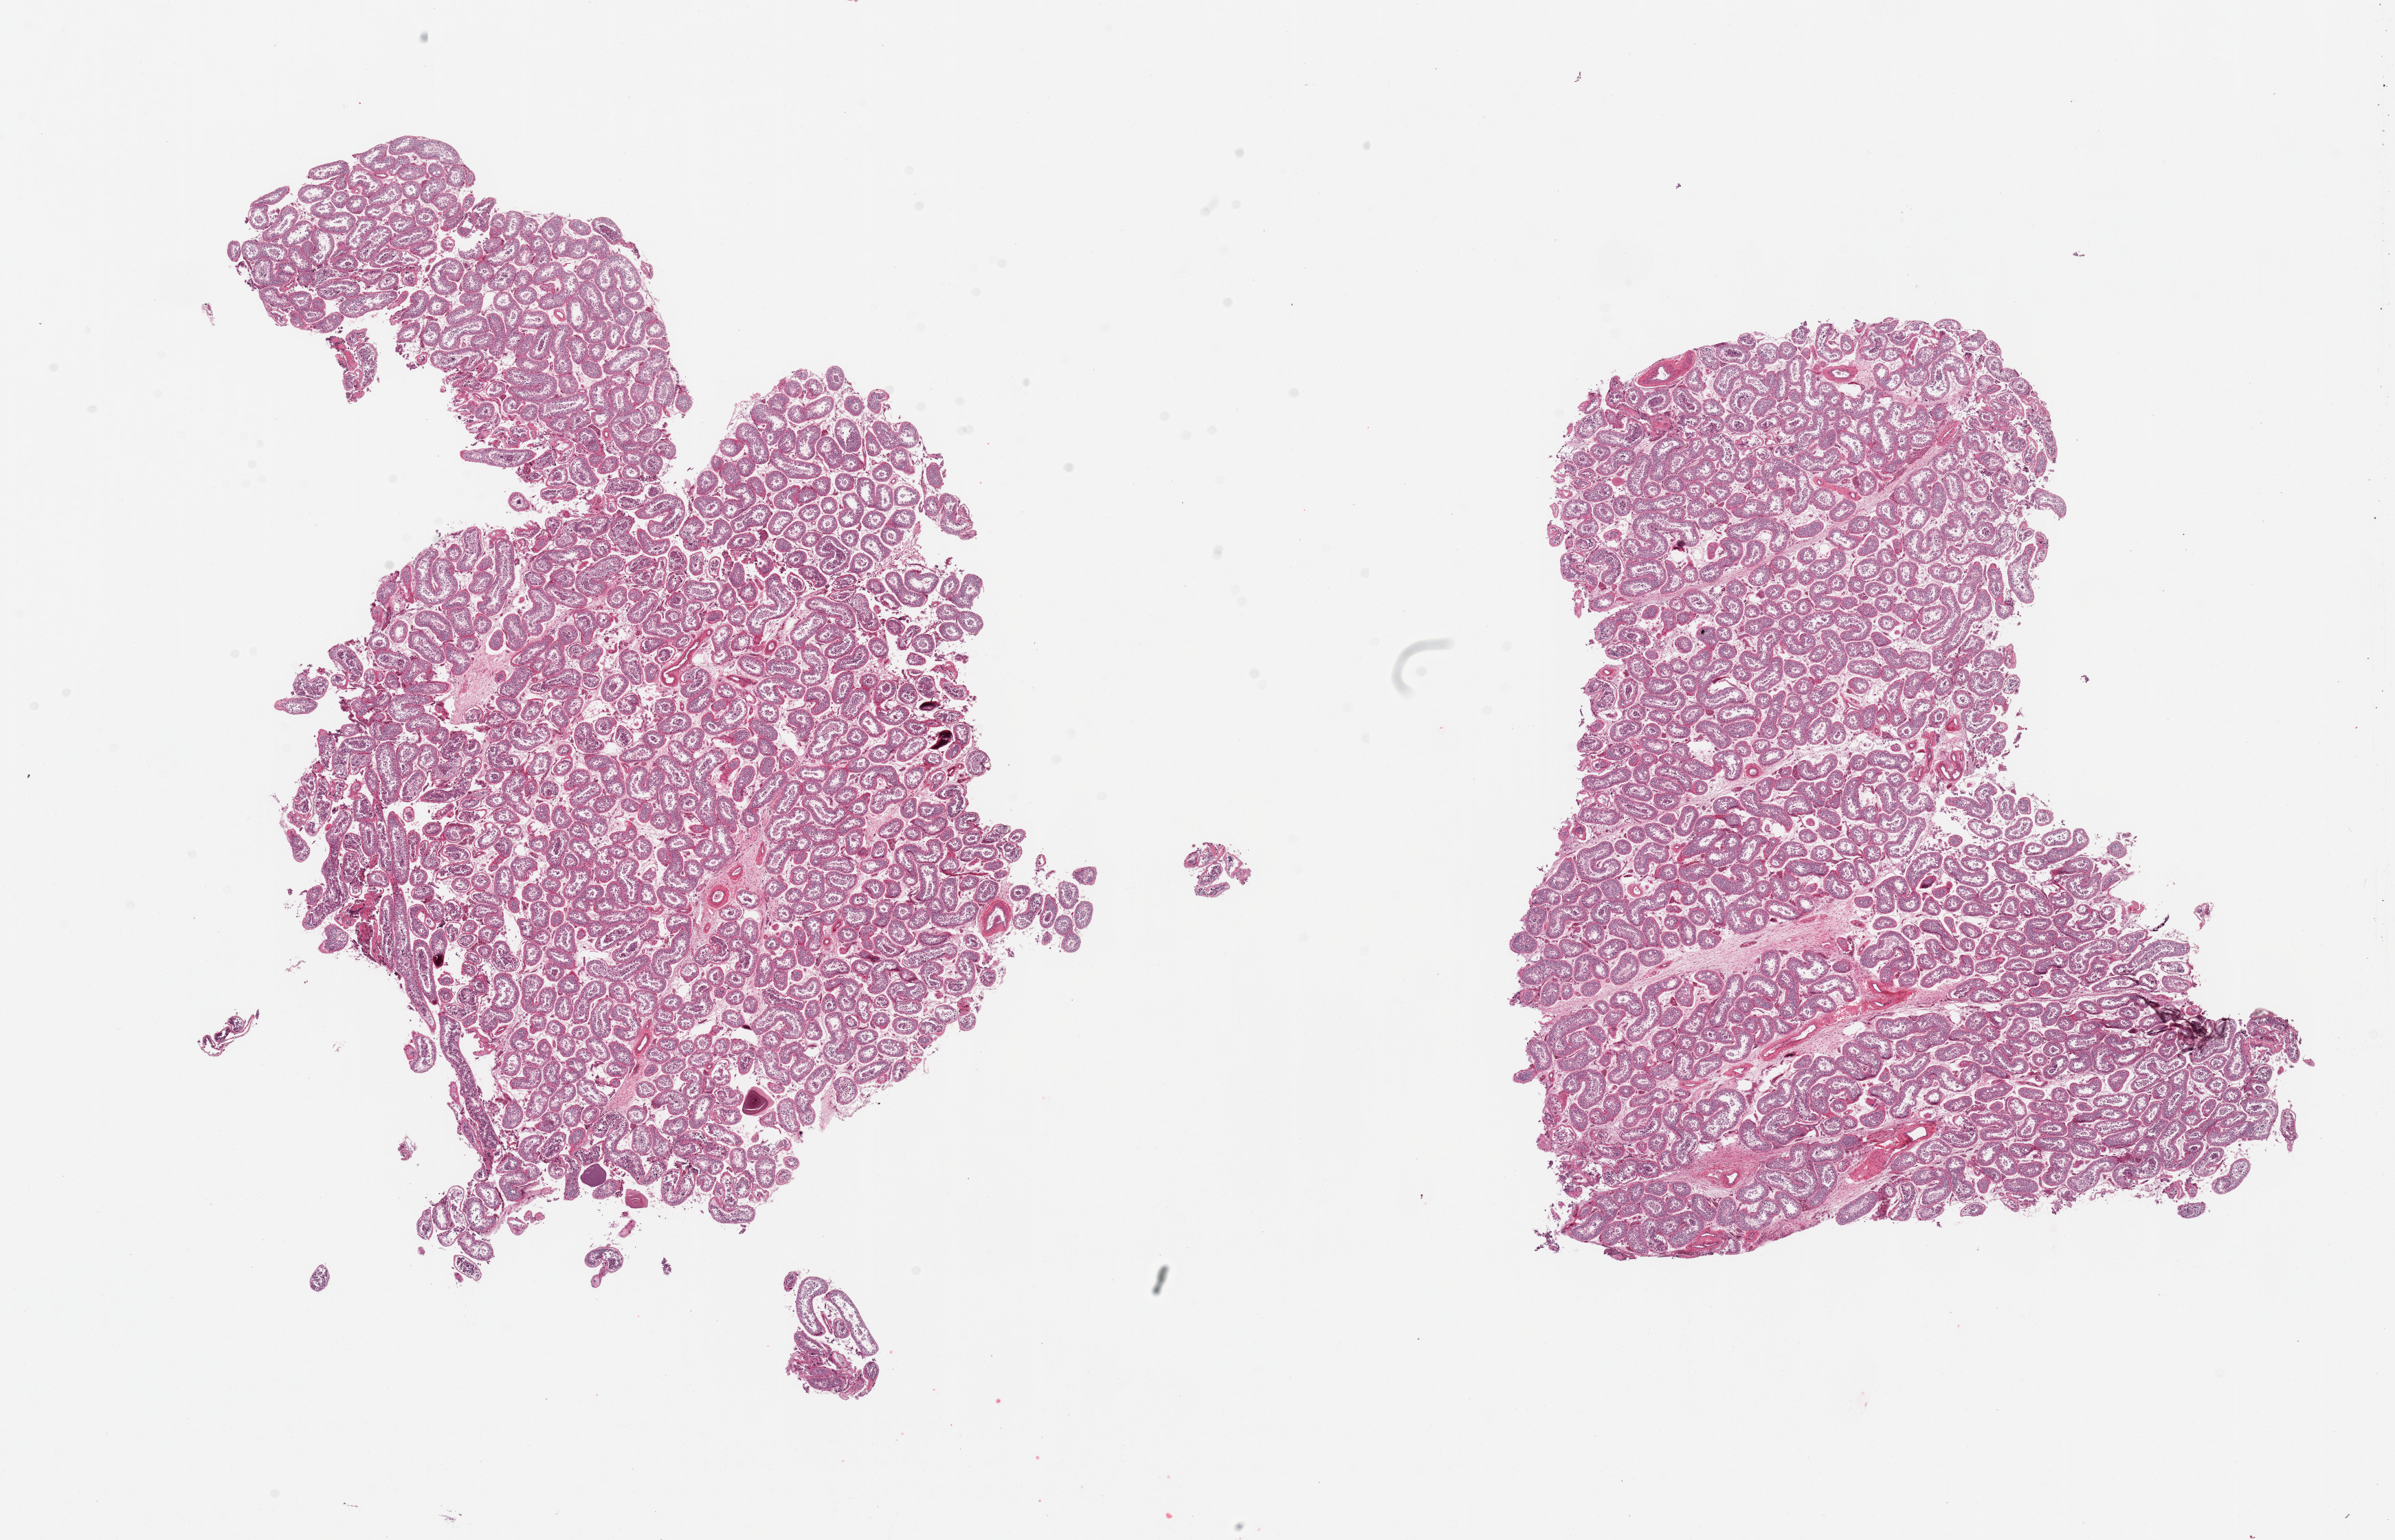
Hematoxylin and eosin (H&E) whole-slide image — whole scanned area (about 27.6 x 17.7 mm, from a 20x scan) shown as a low-resolution overview; PAXgene-fixed paraffin-embedded (PFPE) section; section of testis (target tissue); tissue donor sample. Male donor.
Reviewer comment on this tissue sample: 2 pieces; spermatogenesis is present.